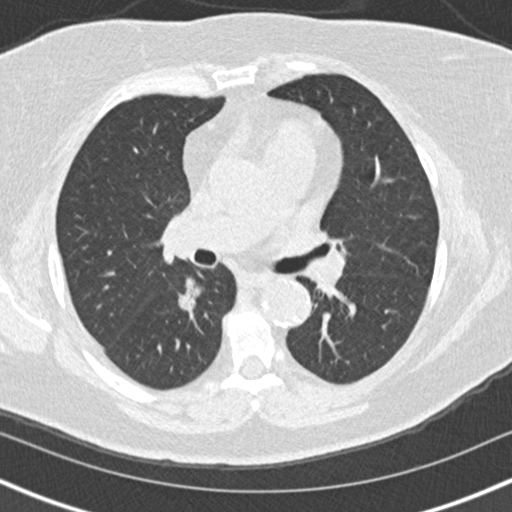
Low-dose screening chest CT, one axial slice. Position 91 of 152 along the scan axis. Reconstruction kernel B30f. 120 kVp. Lung window (W 1500 / L -600 HU). 2 mm slice thickness. 512 × 512 image matrix, field of view 320 × 320 mm.
Outlined on this slice (outlined manually by an expert reader):
- lesion 1 (tumor, lower lobe of right lung): bounding box <178,278,201,311> (left, top, right, bottom; pixels)